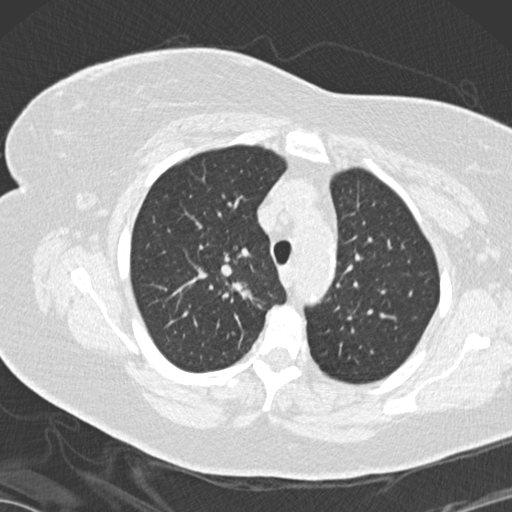
Low-dose screening chest CT, one axial slice; slice 111 of 146 in the series (ordered by position); 120 kVp; lung window (W 1500 / L -600 HU); 512 × 512 image matrix, field of view 350 × 350 mm.
Annotated regions visible in this slice (outlined manually by an expert reader):
- lesion 1 (tumor, upper lobe of right lung): bounding box [x1, y1, x2, y2] px = [223, 282, 251, 299]